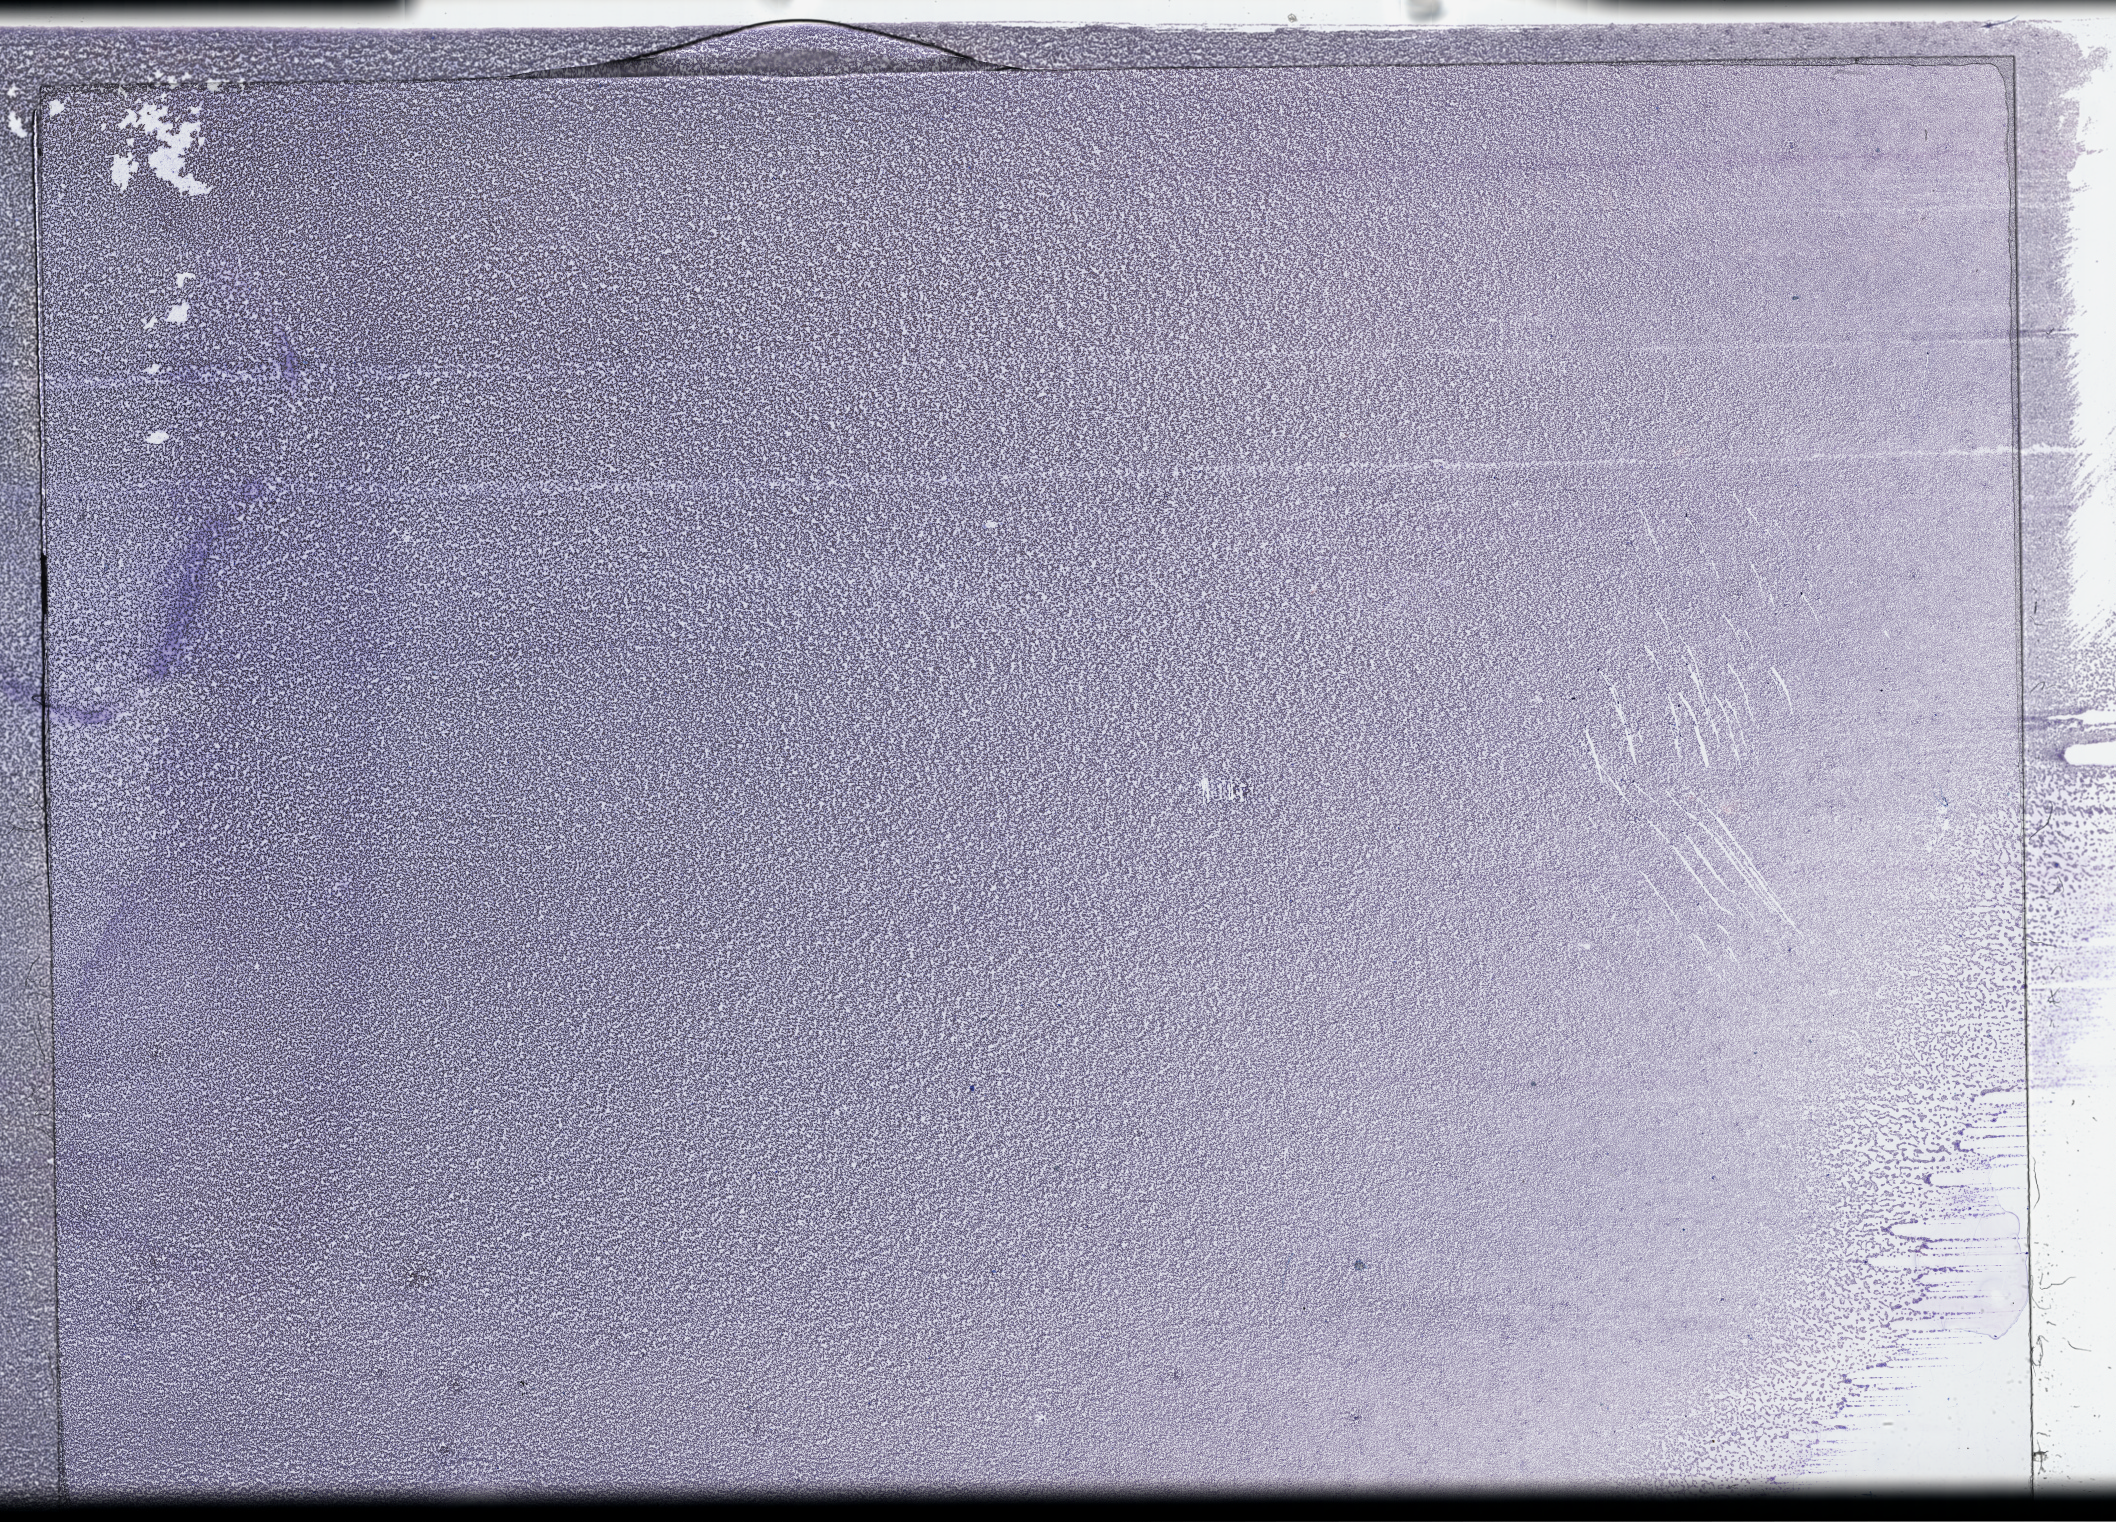
Digitized Hematoxylin and eosin (H&E) stained tissue section (whole slide) — shown as a low-resolution overview of the whole scanned area (about 34.2 x 24.6 mm, acquisition: 40x scan), peripheral blood (leukaemic) sample. Patient: male, age 71 years.
• FAB classification: M2
• diagnosis: Acute Myeloid Leukemia